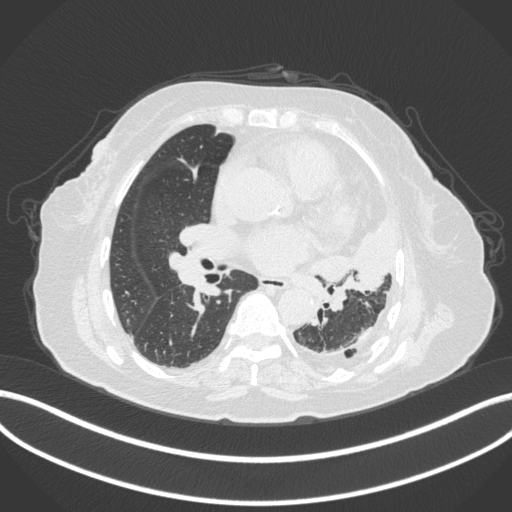
Chest CT, one axial slice. Slice 185 of 399 in the series (ordered by position). 120 kVp. Lung window (W 1500 / L -600 HU). 512 × 512 image matrix. Patient: female, 75 years. From the clinical record (not read from this slice): clinical TNM (as recorded): T3 N3 M1.
Annotated regions visible in this slice (bounding box drawn by a radiologist):
- lung tumour (recorded histology: adenocarcinoma): bounding box (x1, y1, x2, y2) in pixels: (294, 206, 401, 301)